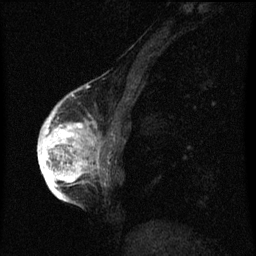
Breast MRI (dynamic contrast-enhanced), one sagittal slice; position 21 of 60 along the scan axis; dynamic contrast-enhanced series, image 2 of 3 at this slice position (ordered by acquisition); 1.5 T; TE 4.2 ms, TR 8 ms; 256 × 256 image matrix, field of view 180 × 180 mm. Patient: female, 56 years.
Annotated regions visible in this slice (semi-automatic segmentation, software-assisted and operator-edited):
- analysis volume of interest (the breast-tissue region the enhancement analysis was run in; not a lesion): bounding box <42,110,103,193> (left, top, right, bottom; pixels)
- tumour enhancement mask (voxels above the 70 % enhancement threshold inside the analysis volume of interest): <42,110,99,193>